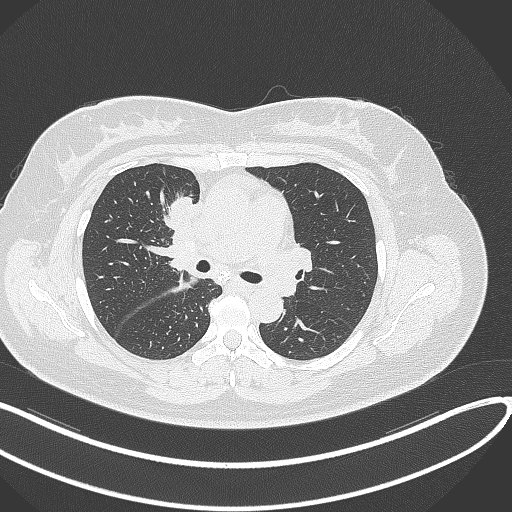
Chest CT, one axial slice. Position 167 of 303 along the scan axis. 120 kVp. Lung window (W 1500 / L -600 HU). 1 mm slice thickness. 512 × 512 image matrix, field of view 400 × 400 mm. Patient: female, 46 years. From the clinical record (not read from this slice): clinical TNM (as recorded): T2a N1 M0.
Structures marked on this image (bounding box drawn by a radiologist):
- lung tumour (recorded histology: adenocarcinoma): box from (x=165, y=195) to (x=195, y=236) px